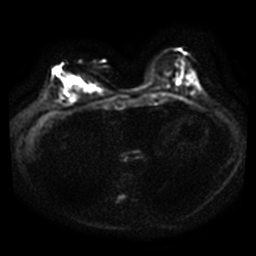
Breast MRI, one axial slice; diffusion-weighted series; image 2 of 4 stored at this slice position (different b-values; order by instance number); 3 T; 5 mm slice thickness; 256 × 256 image matrix, field of view 340 × 340 mm. Female patient.
Outlined on this slice (outlined manually by an expert reader):
- tumour on diffusion-weighted imaging: box from (x=55, y=67) to (x=80, y=88) px